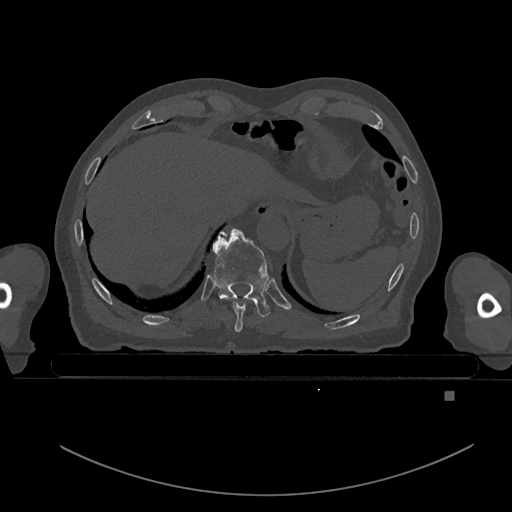
CT including the spine, one axial slice. Slice 110 of 969 in the series (ordered by position). Bone window (W 1800 / L 400 HU). 0.5 mm slice thickness. 512 × 512 image matrix, field of view 456 × 456 mm. Male patient, age 82 years. From the clinical record (not read from this slice): primary cancer: prostate.
Outlined on this slice (semi-automatic segmentation, software-assisted and operator-edited):
- T10 vertebra: bounding box [x1, y1, x2, y2] px = [212, 228, 271, 317]
- T9 vertebra: [223, 234, 247, 332]